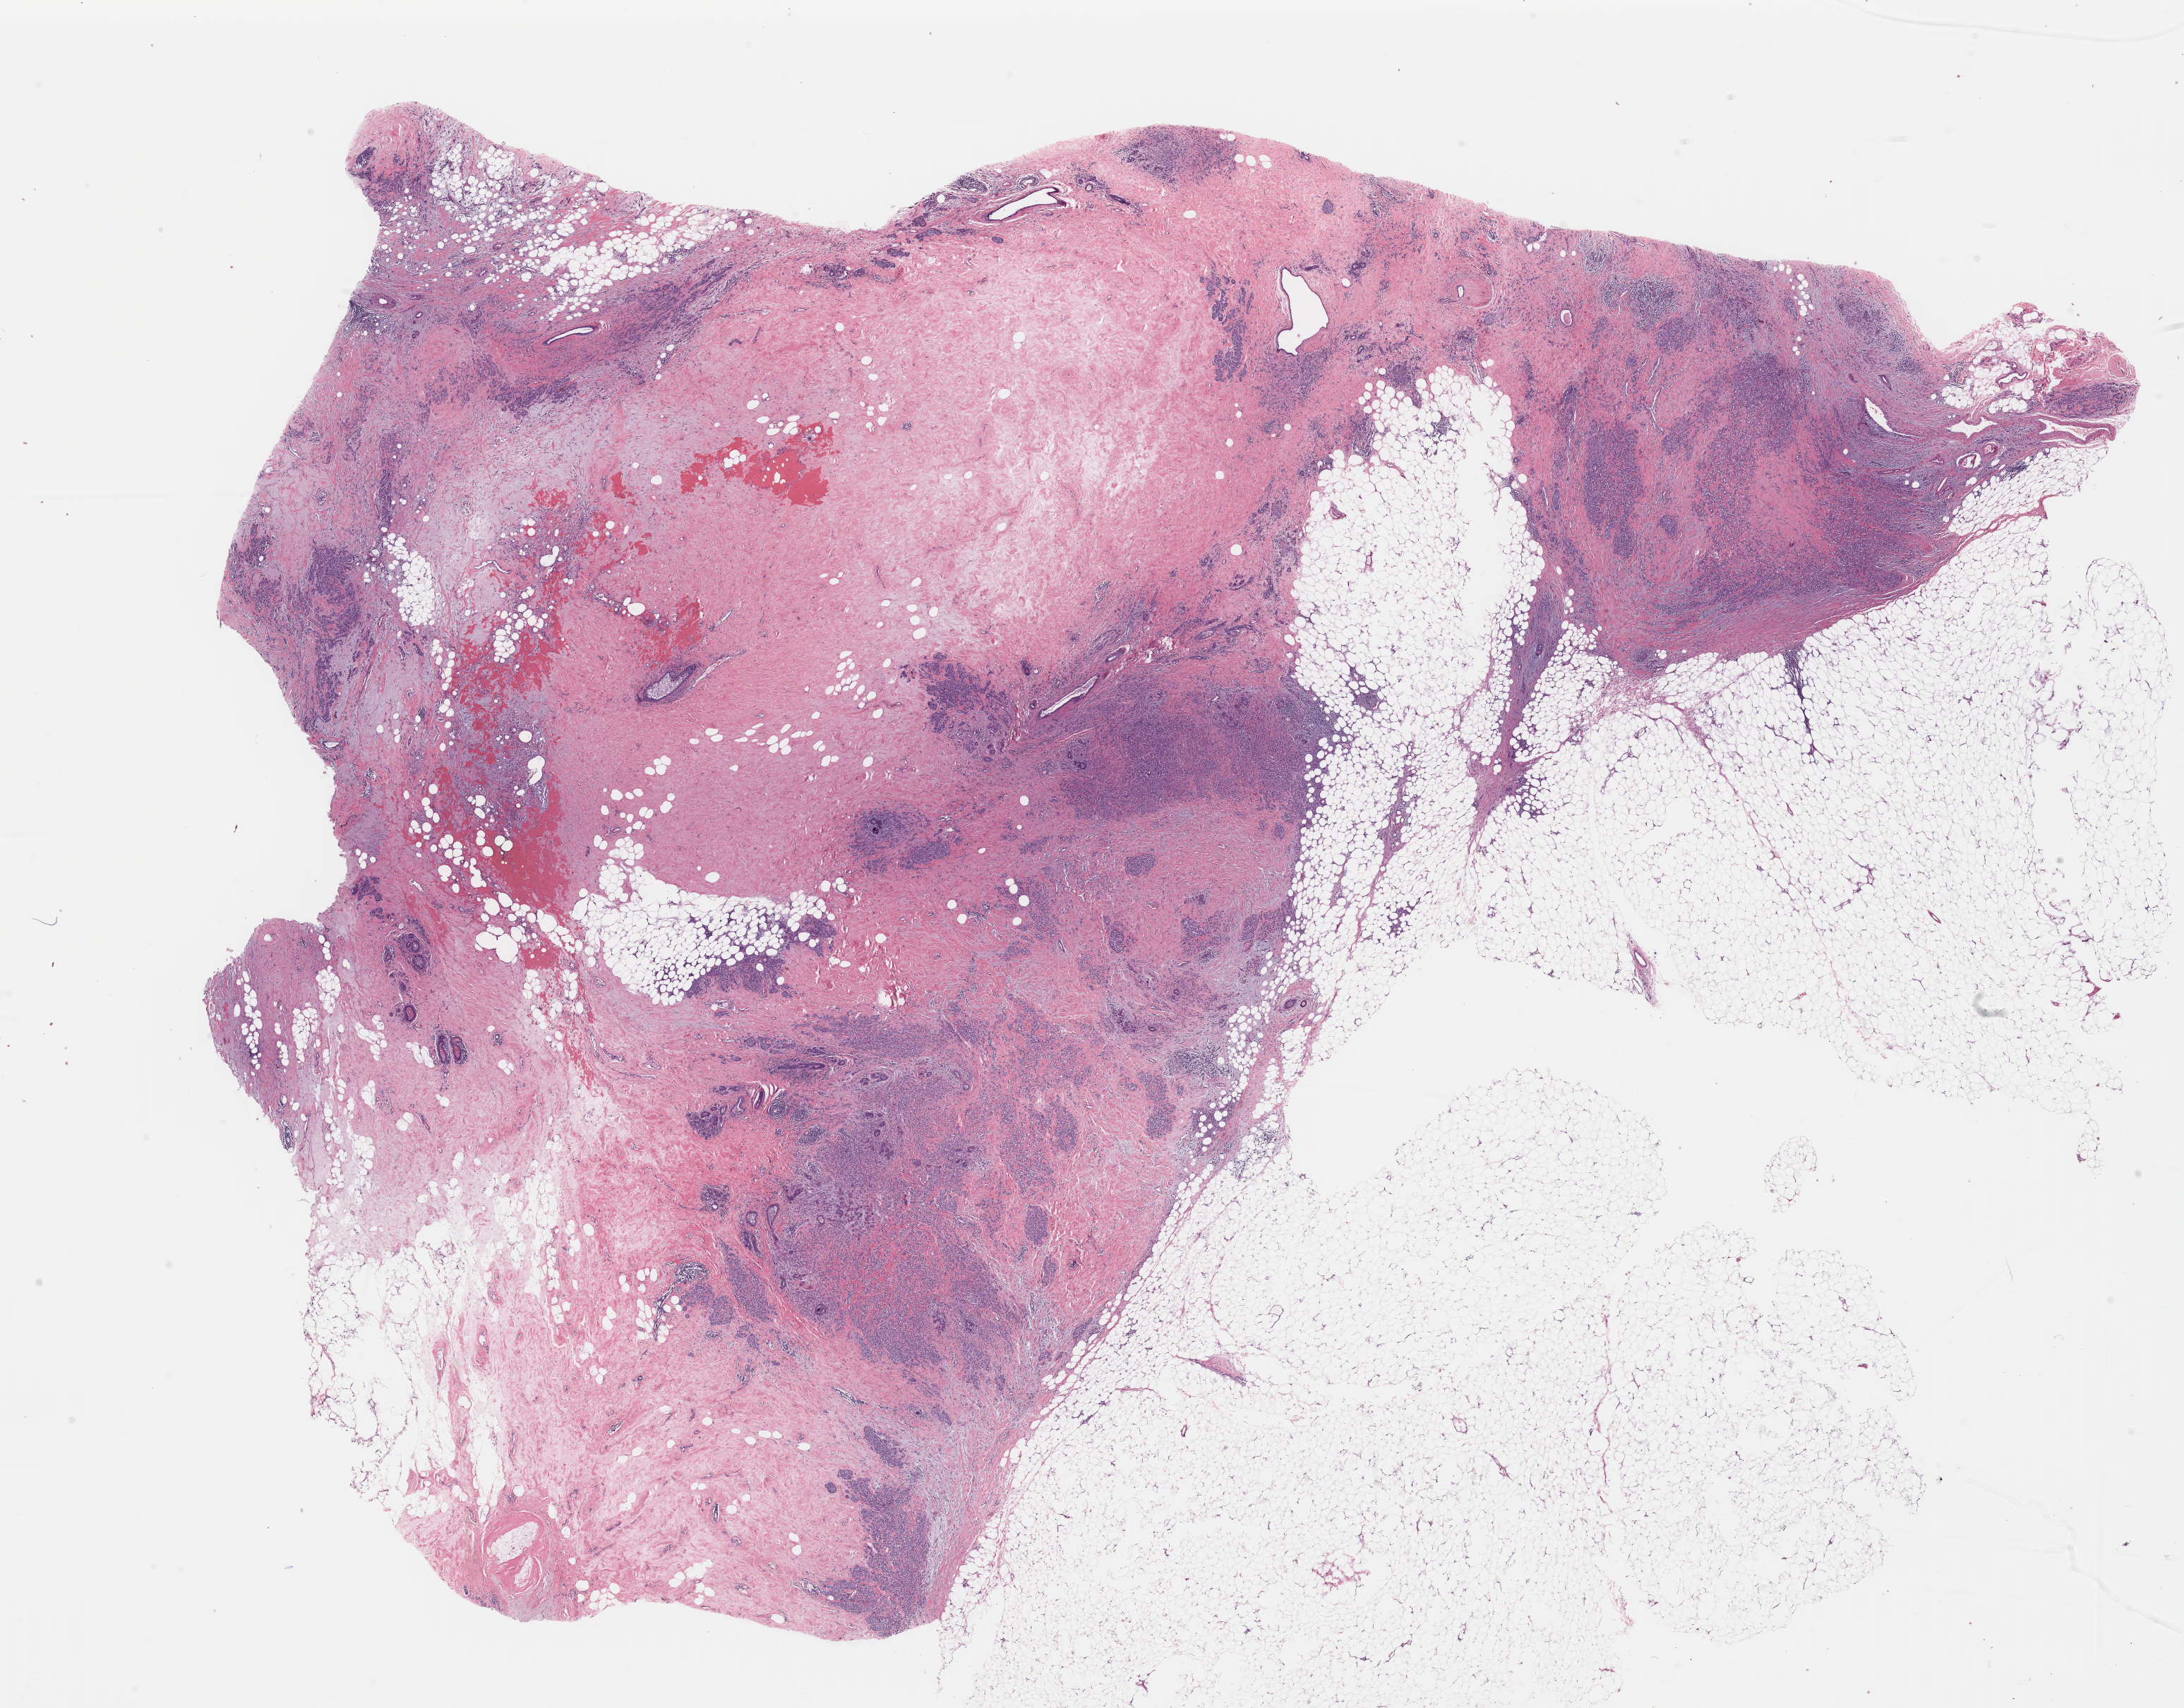
Whole-slide histology image, H&E — shown as a low-resolution overview of the whole scanned area (about 24.4 x 19.1 mm, from a 40x scan); formalin-fixed paraffin-embedded (FFPE) diagnostic section; primary tumour sample from the breast. Patient: female, age at initial diagnosis 62 years.
Histologic diagnosis: Infiltrating lobular mixed with other types of carcinoma. Laterality: right. AJCC pathologic stage: IIIA.